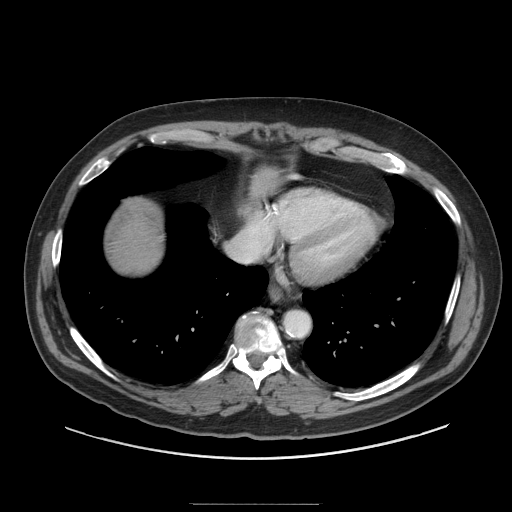
Contrast-enhanced abdominal CT (liver protocol), one axial slice. Slice 85 of 91 in the series (ordered by position). Reconstruction kernel STANDARD. 140 kVp. Soft-tissue window (W 400 / L 40 HU). 512 × 512 image matrix, field of view 440 × 440 mm. Case-level facts recorded for this patient, not image findings: diagnosis: hepatocellular carcinoma (patient treated with transarterial chemoembolisation; whether this scan precedes or follows treatment is not stated here); TNM stage (as recorded): Stage-I; Child-Pugh class: A; tumour differentiation: well differentiated; tumour size: 4 cm.
Annotated regions visible in this slice (semi-automatically segmented with operator editing):
- liver parenchyma outside the tumour (the mass and vessels are separate outlines, so this box may not span the whole liver): bounding box <106,198,164,274> (left, top, right, bottom; pixels)